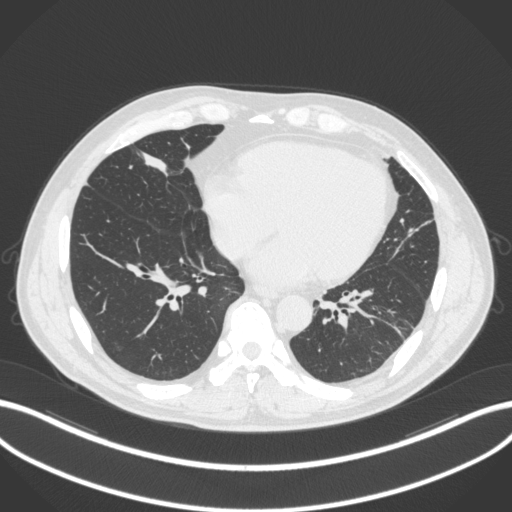
Chest CT, one axial slice. Position 93 of 399 along the scan axis. Reconstruction kernel B31f. 120 kVp. Lung window (W 1500 / L -600 HU). 1 mm slice thickness. 512 × 512 image matrix, field of view 400 × 400 mm. Male patient, age 59 years. From the clinical record (not read from this slice): clinical TNM (as recorded): T2a N1 M0.
Annotated regions visible in this slice (rectangle marked by the reading radiologist):
- lung tumour (recorded histology: adenocarcinoma): box from (x=135, y=146) to (x=176, y=185) px